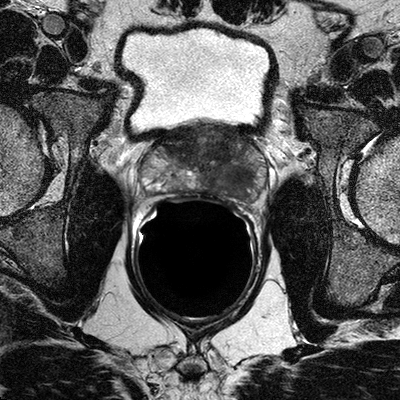
Multiparametric prostate MRI examination; 3 images, each a single mid-volume slice chosen by position (not for content). Treatment context recorded for this patient: No surgery, Casodex, Lupron and XRT.
Image 1: T2-weighted axial slice, series "T2W_TSE_AX", slice 17 of 32.
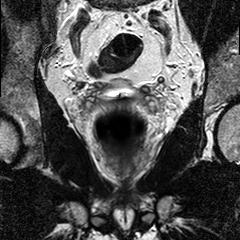
Image 2: T2-weighted coronal slice, series "T2W_TSE_COR", slice 13 of 24.
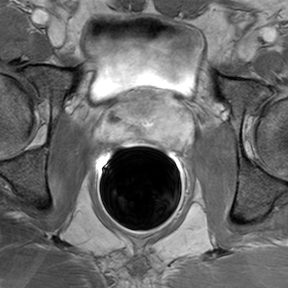
Image 3: axial dynamic contrast-enhanced (DCE) T1-weighted image, slice 17 of 32, dynamic phase 5 of 8.
Radiologist's MRI report for this examination:
FINDINGS: The prostate has a maximal lateral diameter of 5.3 cm, a maximal craniocaudal diameter of 4.0 cm and a maximal AP diameter of 3.0 cm resulting in an estimated gland volume of 33 cc. The zonal anatomy is preserved. There is a large 3.3 x 2.5 x 2.7 tumor seen in the left upper third (base) of the prostate with extracapsular extension posterior lateral into the left neurovascular bundle/recto prostatic angle just below the left seminal vesicles. There is manifest seminal vesicle infiltration (1.4 x 1.4 cm) at the left seminal vesicle base. No evidence for involvement of the right neurovascular bundle. No evidence of involvement of bladder neck and rectal wall. No suspiciously enlarged obturator and iliac lymph nodes; there is a 6 mm rounded very dense left iliac lymph node posterior to the vasa iliaca and superior-lateral to the right seminal vesicles; This does not meet the size criteria of suspiciously enlarged pelvic lymph nodes. IMPRESSION: 1) 3.3 cm left prostate tumor at the base with manifest (1.4cm) left seminal vesicles infiltration and extraglandular extension into the left recto-prostatic angle at the base. 2) Indeterminate 6 mm left iliac lymph node.